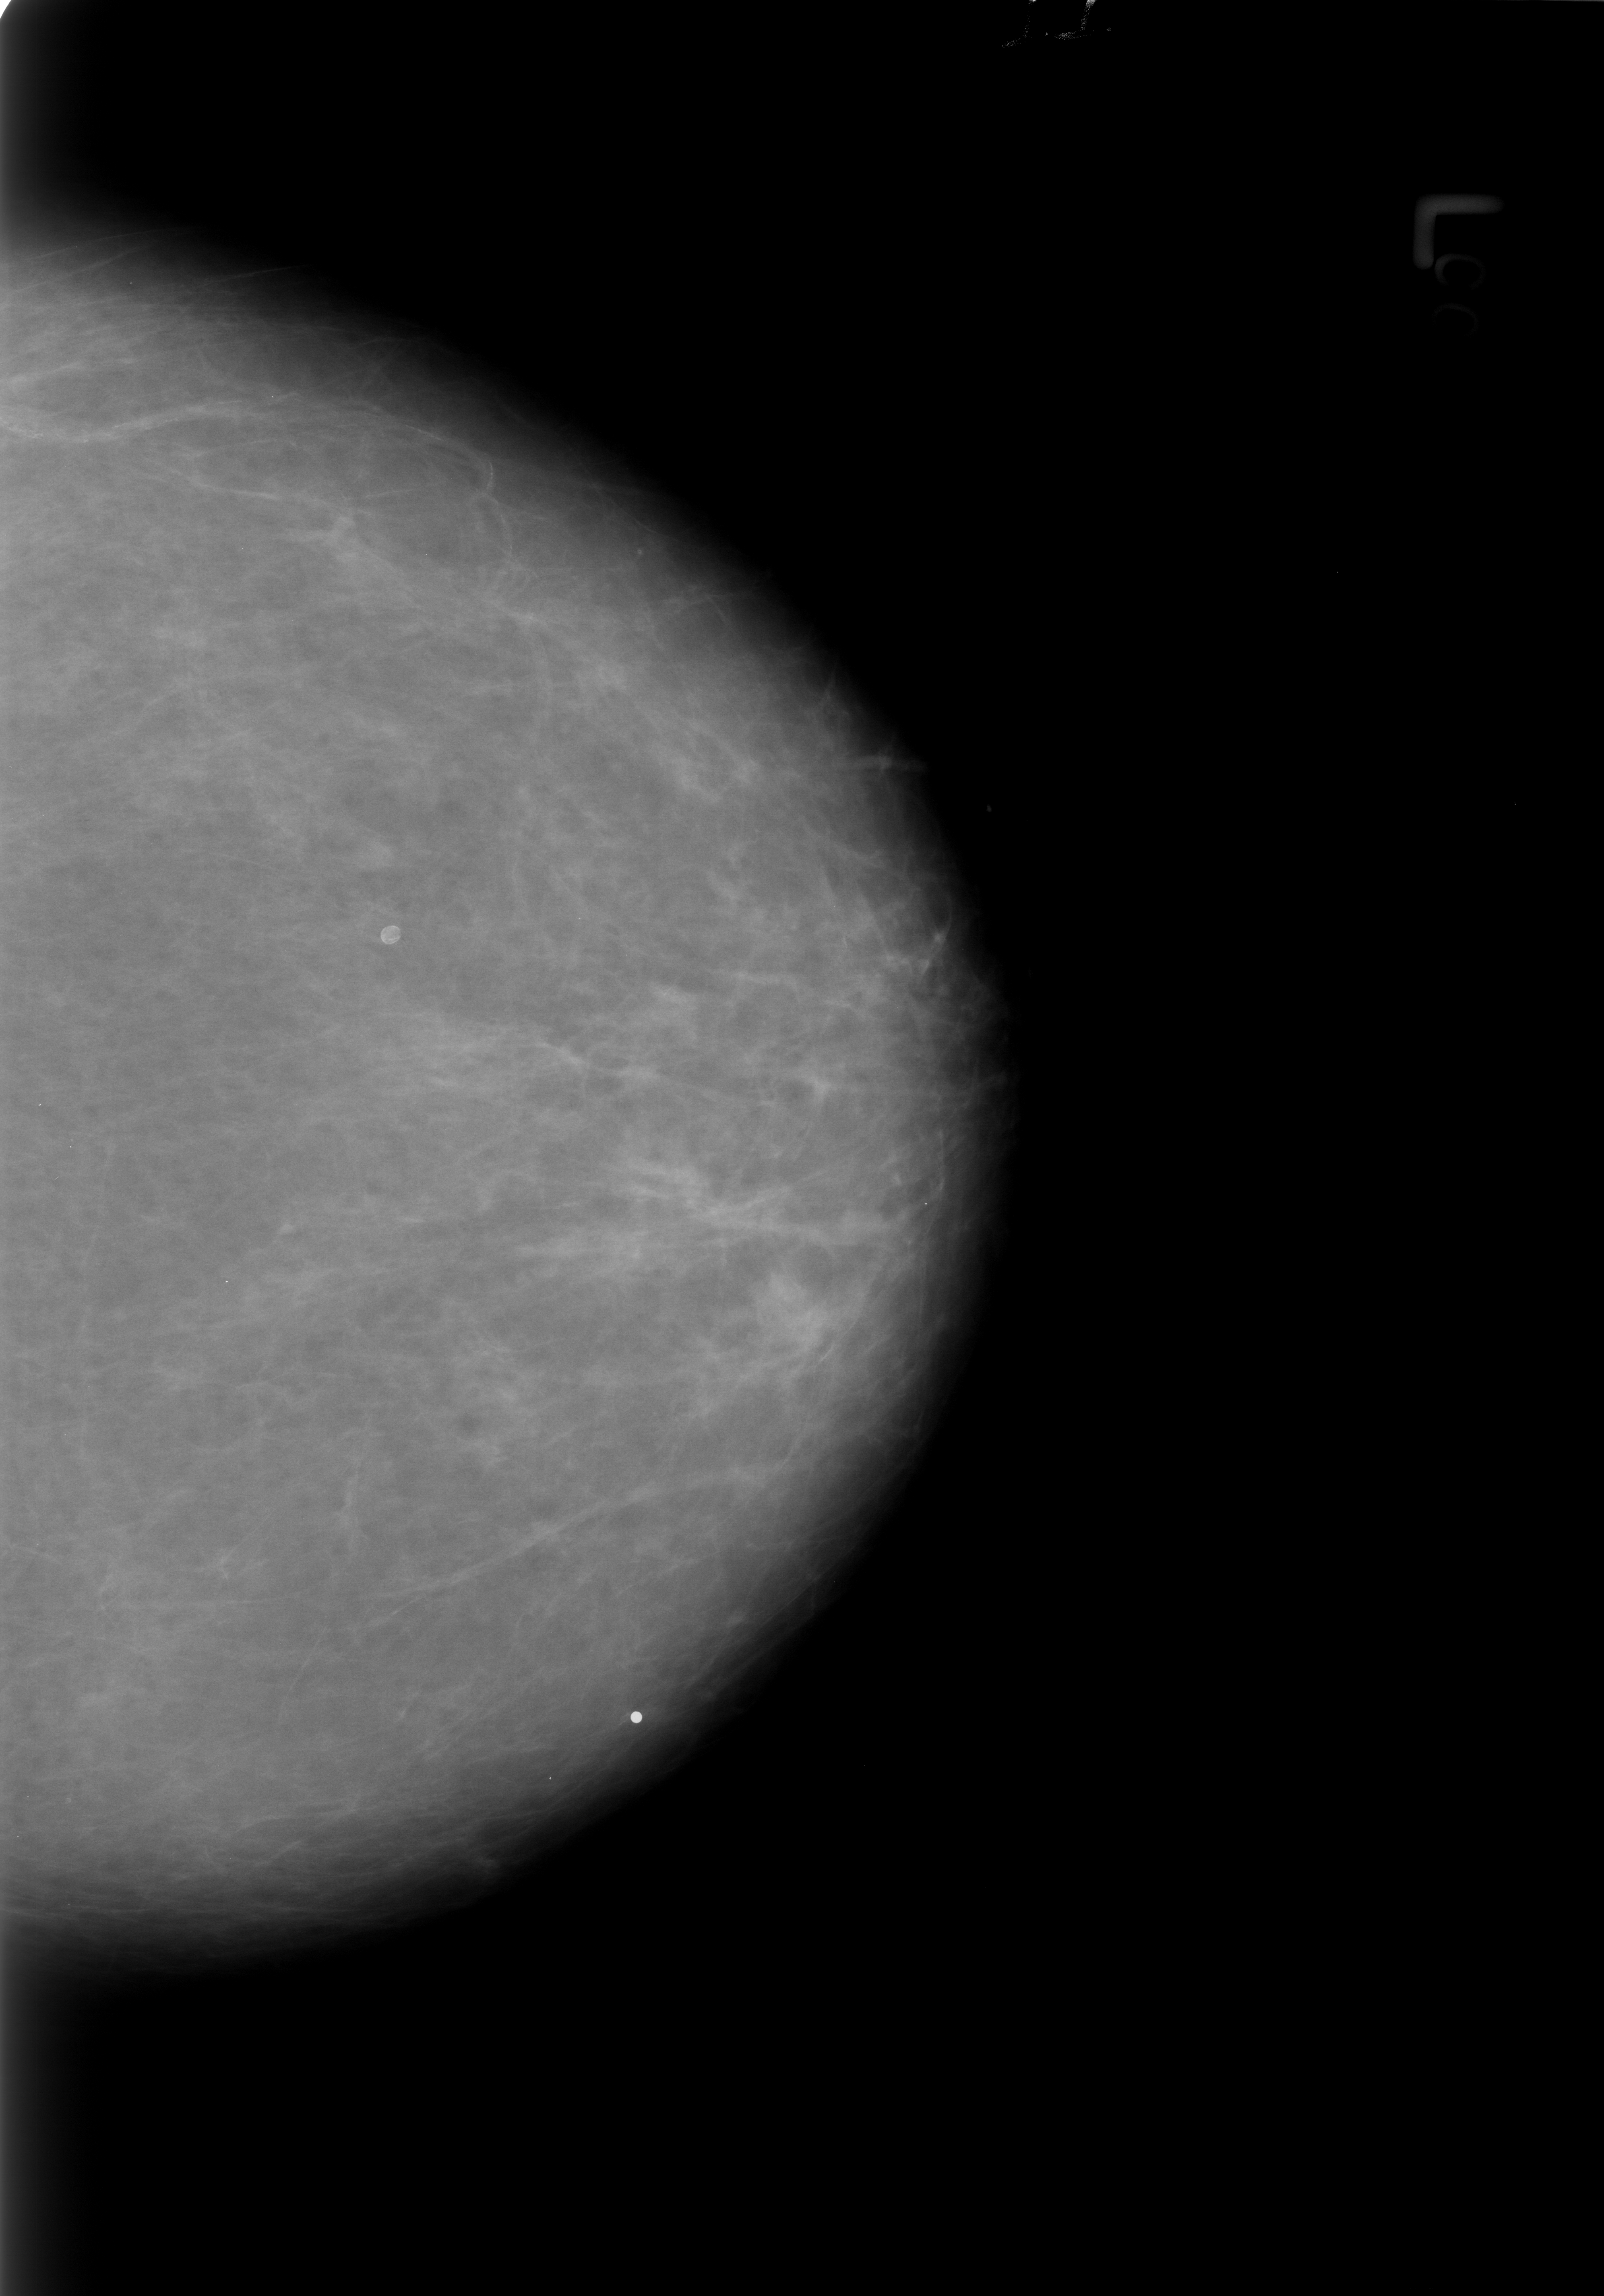
Mammogram (digitized film); left breast; CC view.
Radiologist-marked abnormalities on this image: calcifications, morphology lucent centered; BI-RADS assessment category 2; benign without callback (not worked up further).